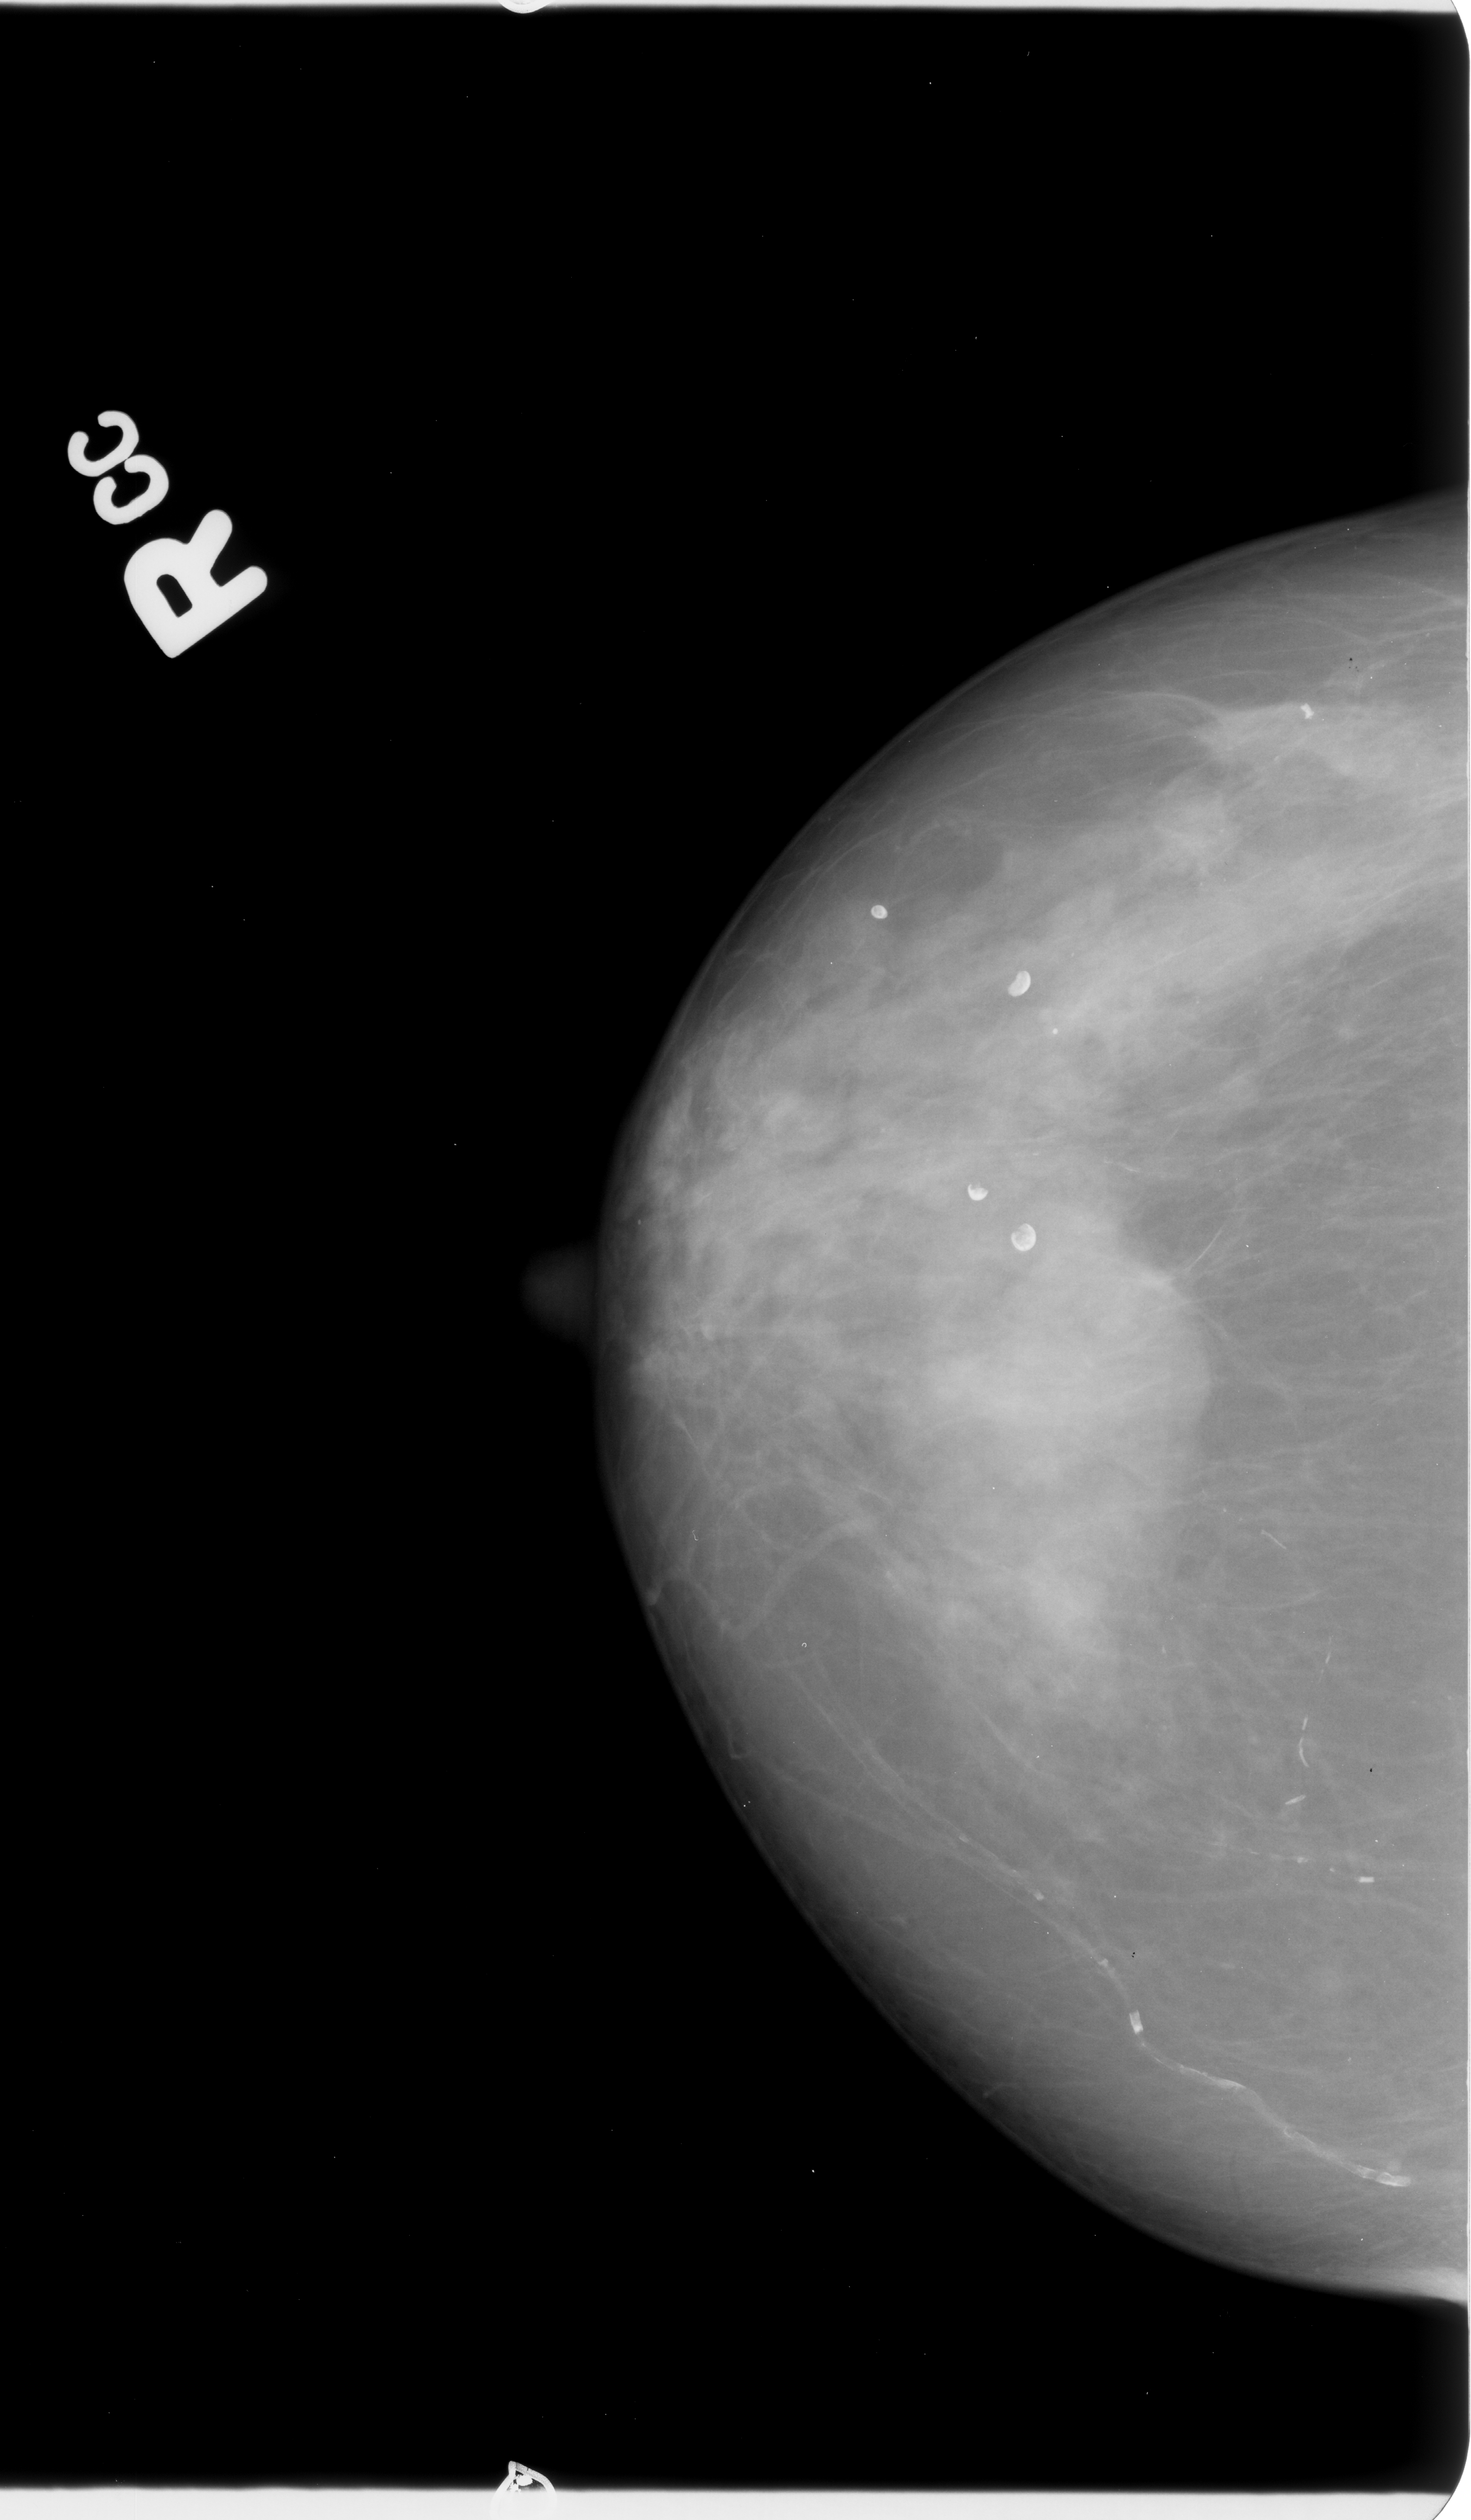
Mammogram (digitized film), right breast, CC view, BI-RADS breast density category 3 (scale 1–4).
Finding: mass, shape oval, margins circumscribed / obscured; BI-RADS assessment category 3; subtlety rating 1 on a 1 (subtle) to 5 (obvious) scale; pathology (as recorded): malignant.